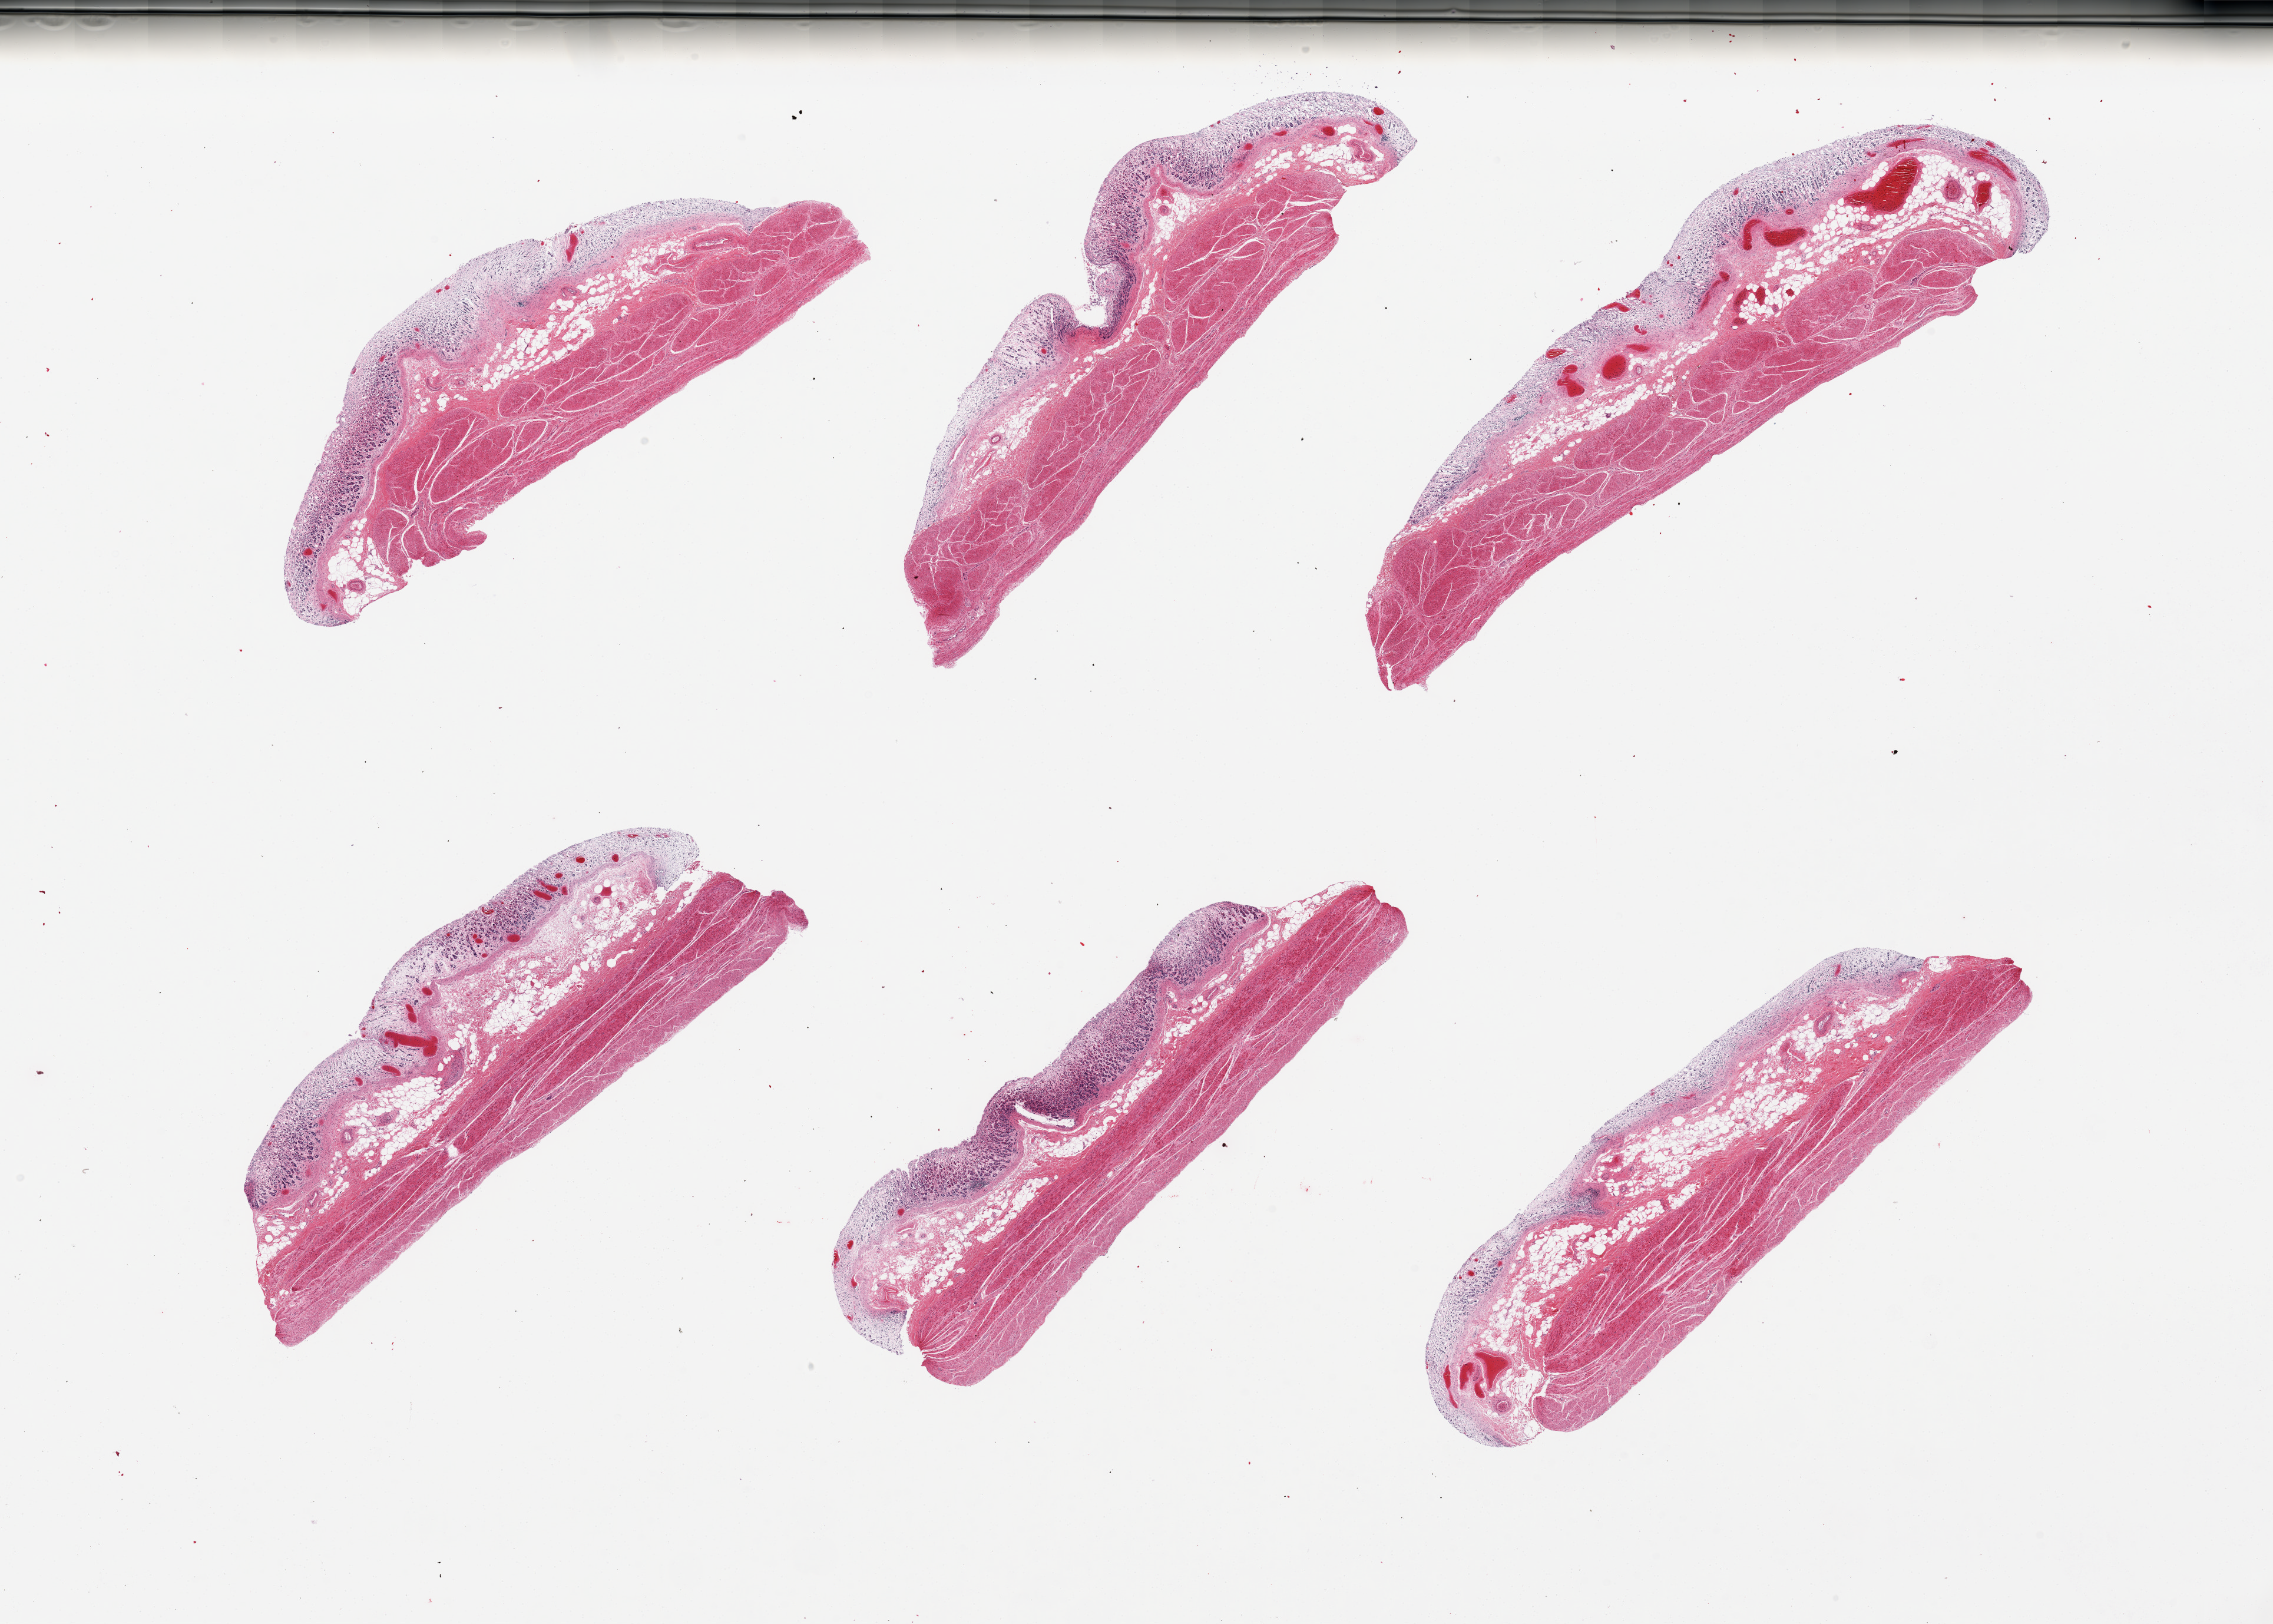
Whole-slide image, H&E stain, low-resolution overview of the scanned area, about 30.5 x 21.8 mm, PAXgene-fixed paraffin-embedded (PFPE) section, section of stomach (target tissue), donor tissue sample.
Reviewer comment on this tissue sample: 6 pieces; mucosa=3, muscle=1 (autolysis).